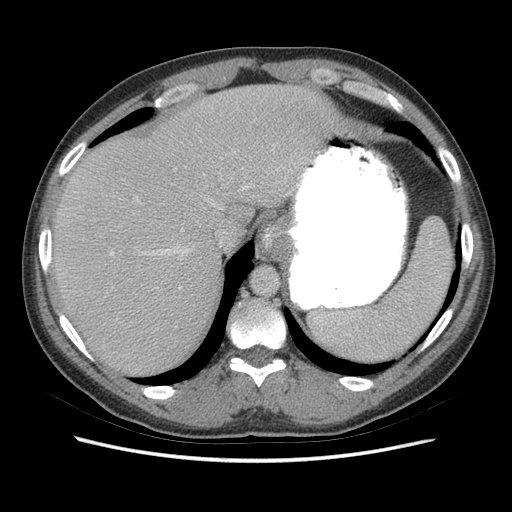
Contrast-enhanced abdominal CT (liver protocol), one axial slice; slice 55 of 73 in the series (ordered by position); reconstruction kernel STANDARD; 140 kVp; soft-tissue window (W 400 / L 40 HU); 2.5 mm slice thickness; 512 × 512 image matrix, field of view 360 × 360 mm. From the clinical record (not read from this slice): diagnosis: hepatocellular carcinoma (patient treated with transarterial chemoembolisation; whether this scan precedes or follows treatment is not stated here); TNM stage (as recorded): Stage-IIIA; Child-Pugh class: A; tumour size: 6.6 cm.
Annotated regions visible in this slice (semi-automatic segmentation, software-assisted and operator-edited):
- liver parenchyma outside the tumour (the mass and vessels are separate outlines, so this box may not span the whole liver): bounding box (x1, y1, x2, y2) in pixels: (52, 84, 346, 376)
- liver vessels: (110, 152, 288, 289)